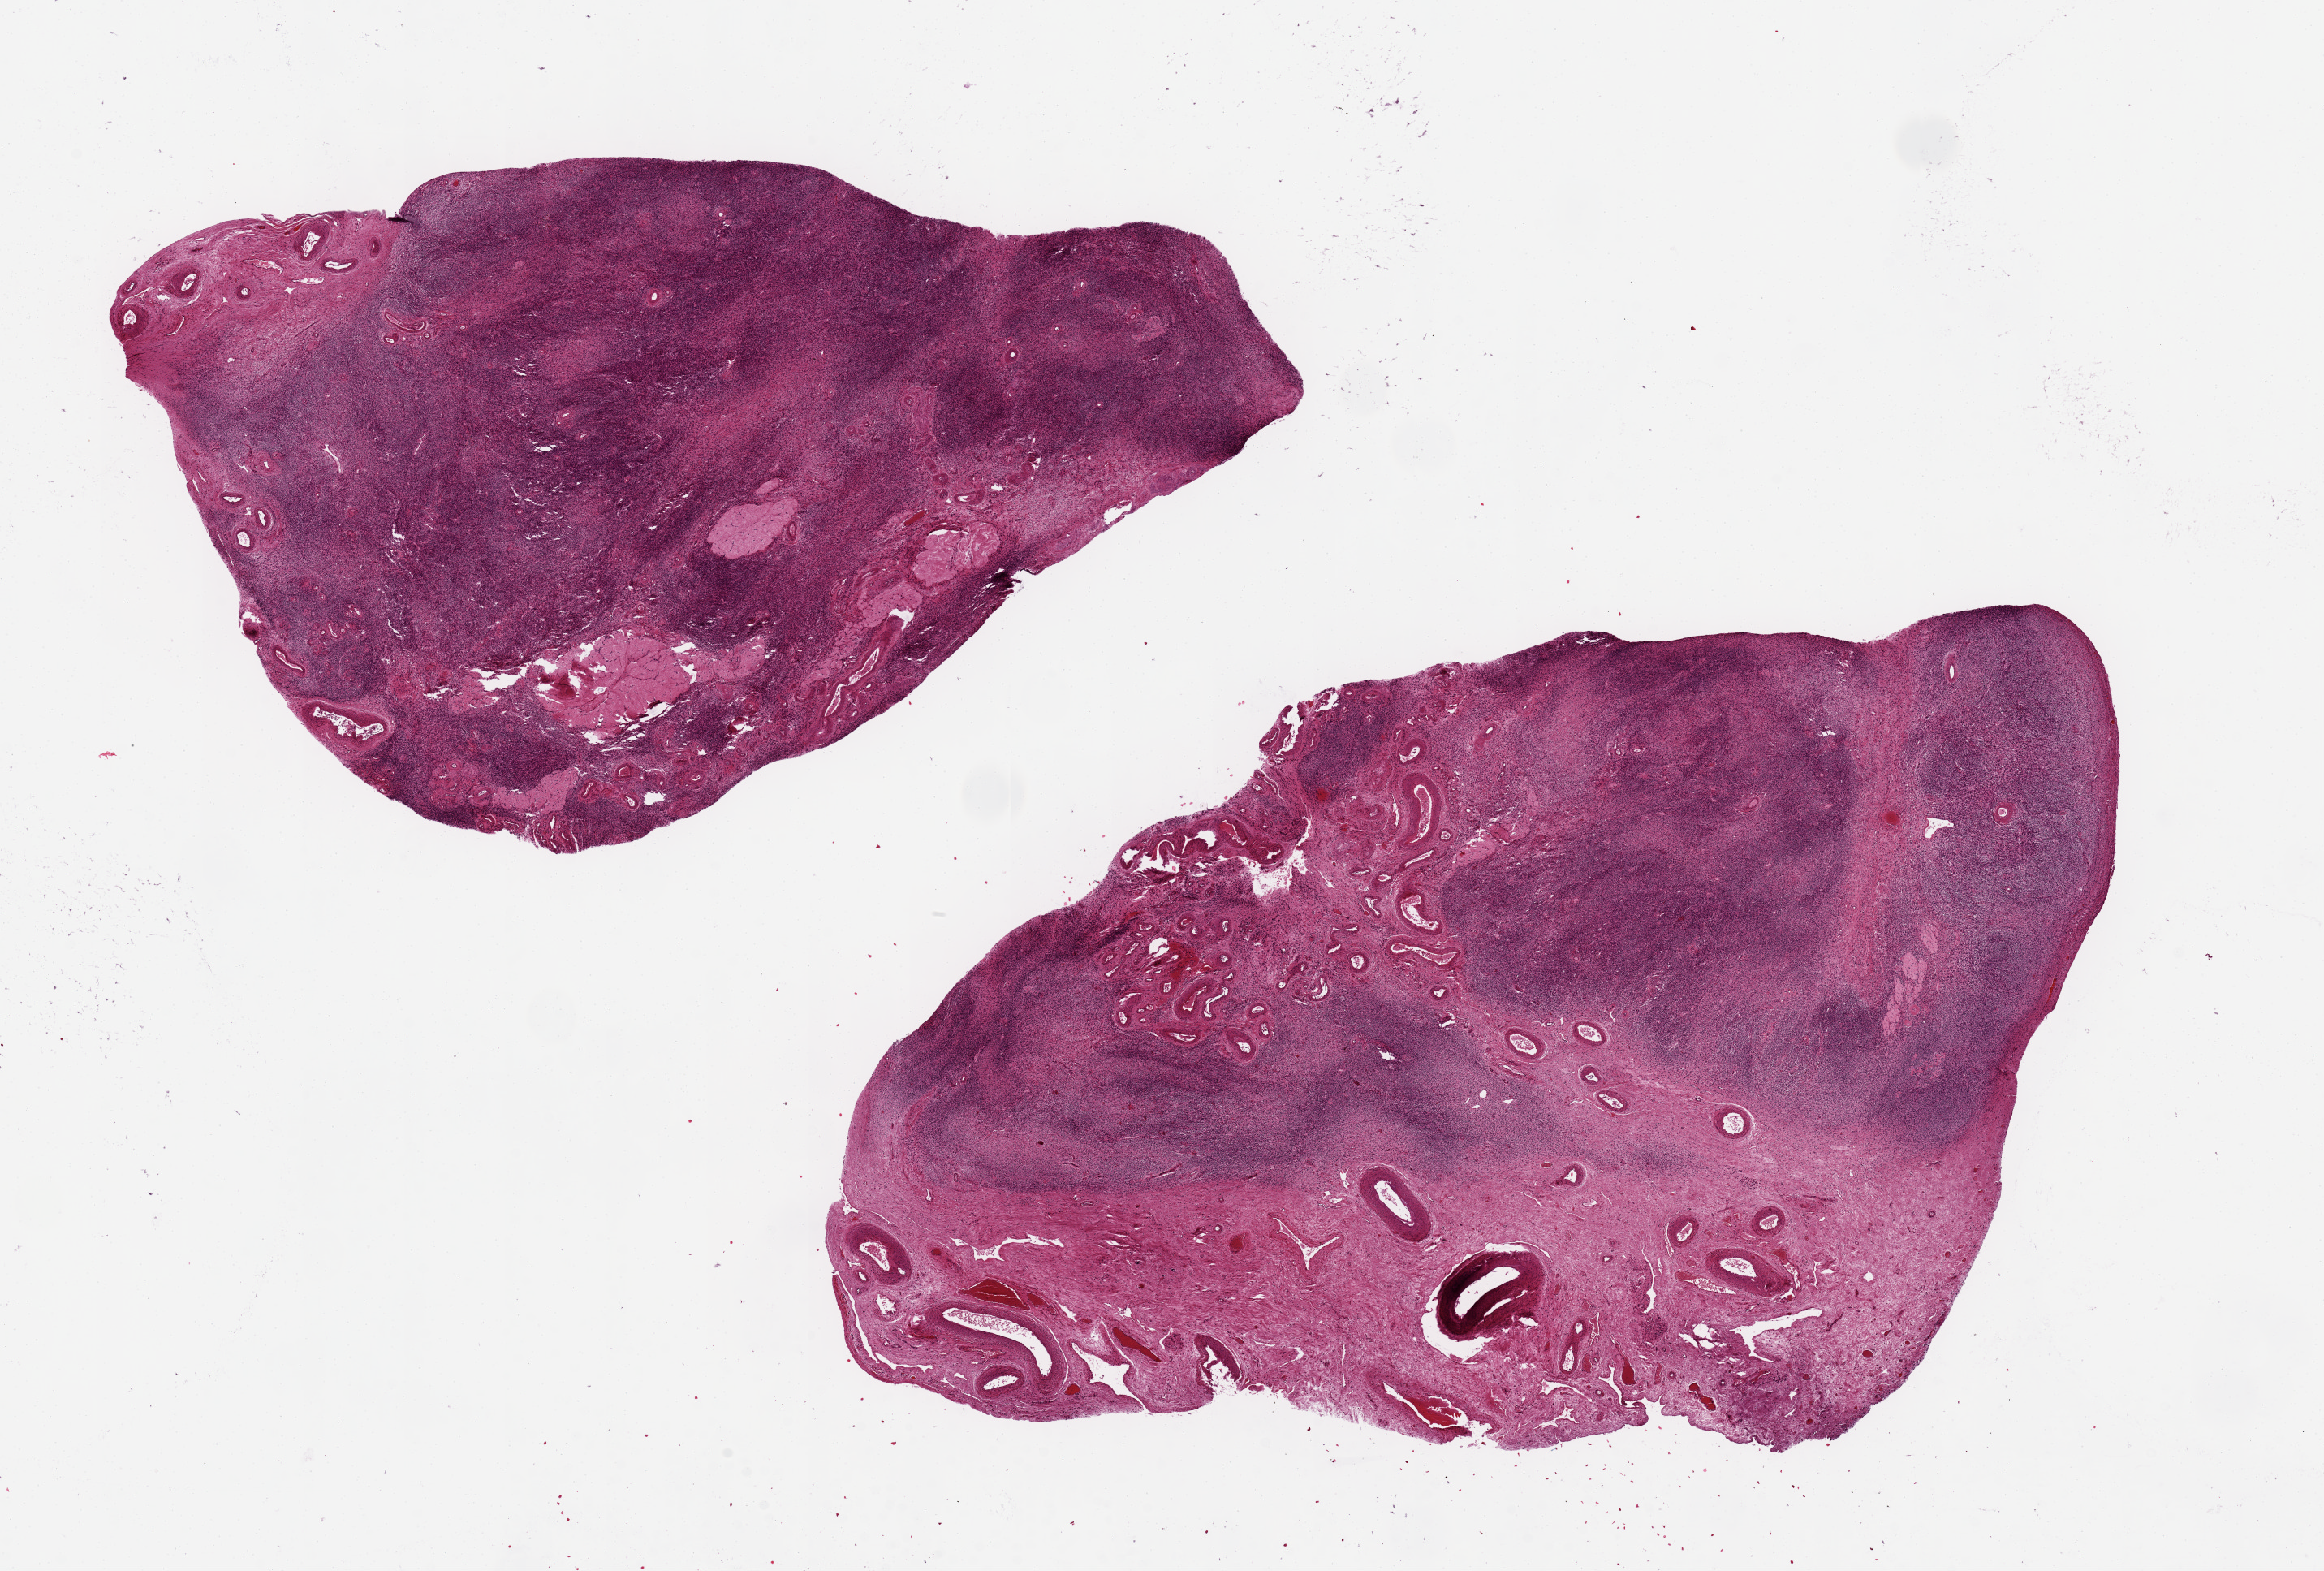
Digitized haematoxylin and eosin-stained section, brightfield, shown as a low-resolution overview of the whole scanned area (about 22.6 x 15.3 mm, from a 20x scan); PAXgene-fixed, paraffin-embedded tissue; section of ovary (target tissue); tissue donor sample. Female donor.
Review note (as recorded): 2 pieces, 11x8 & 10x7 mm; corpora albicans, no ova.